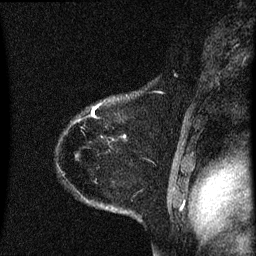
Breast MRI (dynamic contrast-enhanced), one sagittal slice; position 53 of 60 along the scan axis; dynamic contrast-enhanced series, image 2 of 3 at this slice position (ordered by acquisition); 1.5 T; TE 4.2 ms, TR 8.4 ms; 256 × 256 image matrix, field of view 200 × 200 mm. Patient: female, 35 years. From the clinical record (not read from this slice): setting: breast cancer imaged before/during neoadjuvant chemotherapy; receptor status: HER2-positive.
Annotated regions visible in this slice (semi-automatically segmented with operator editing):
- analysis volume of interest (the breast-tissue region the enhancement analysis was run in; not a lesion): bounding box [x1, y1, x2, y2] px = [60, 80, 174, 173]
- tumour enhancement mask (voxels above the 70 % enhancement threshold inside the analysis volume of interest): [91, 104, 101, 117]